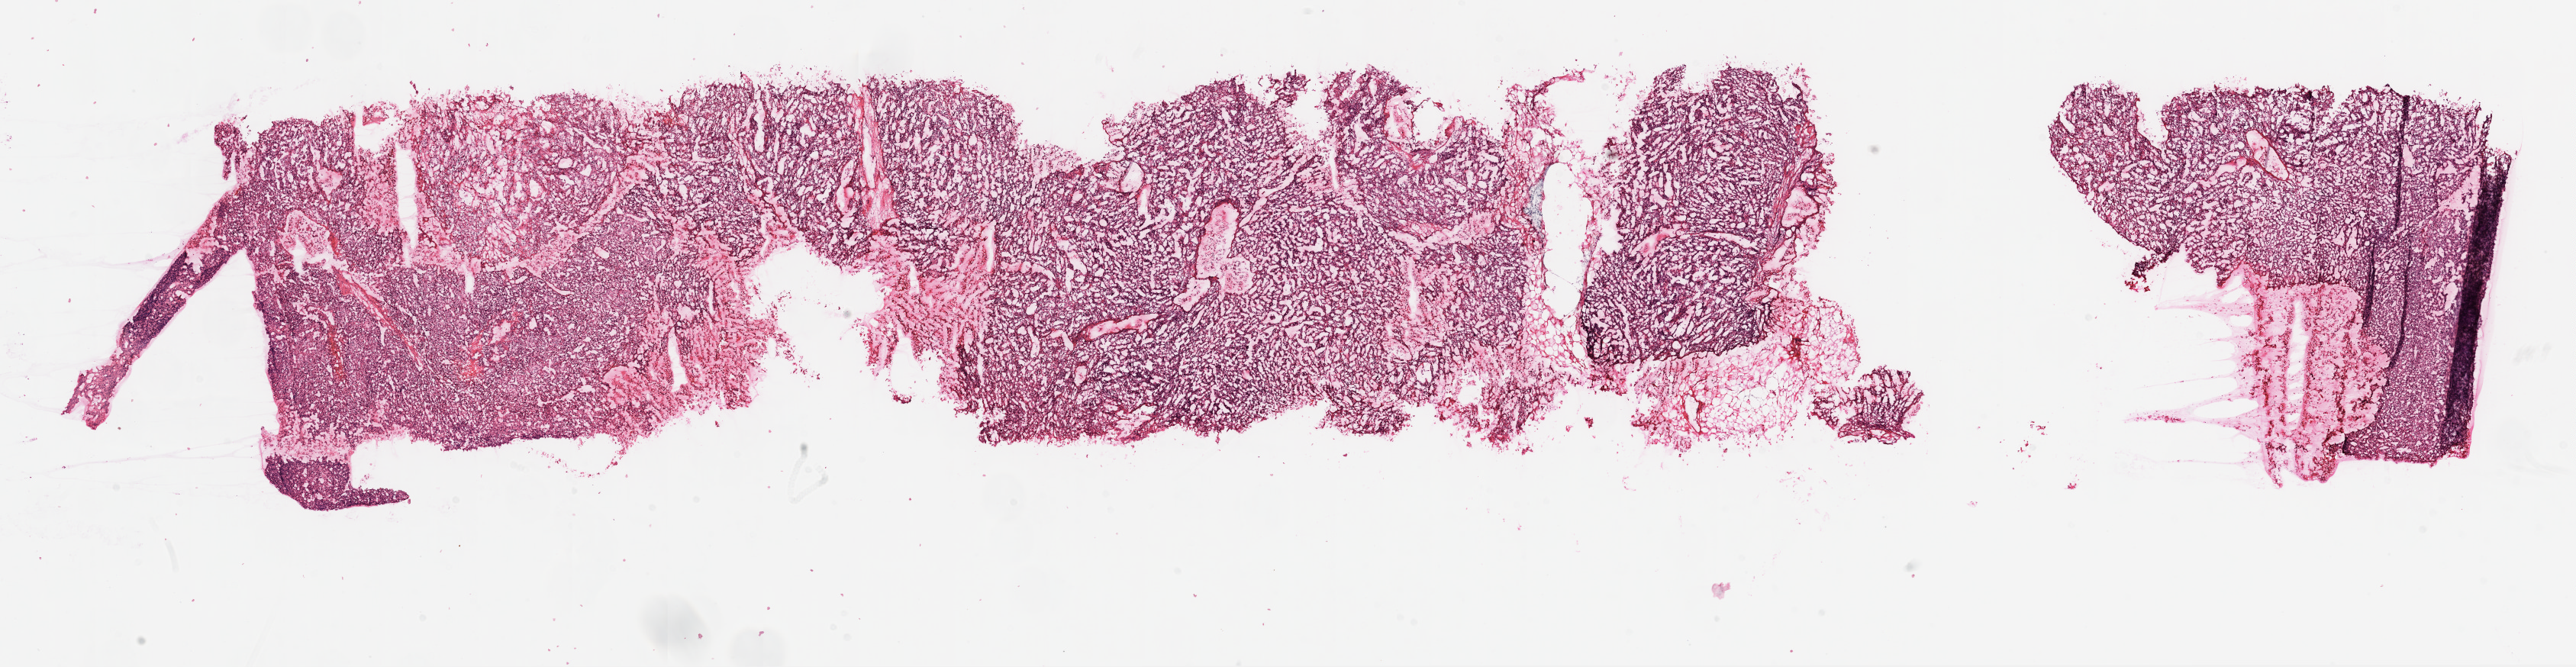
Whole-slide histology image, H&E, whole scanned area (about 27.1 x 7.0 mm, from a 20x scan) shown as a low-resolution overview. Frozen section from the top of the tissue portion. Sample: primary tumour, kidney. Female, age 65 years at initial diagnosis. Histologic grade: G2 (moderately differentiated). Pathologist review of this section (percent, as recorded): tumour cells 90%, tumour nuclei 85%, normal cells 0%, stromal cells 10%, necrosis 0%.
AJCC pathologic stage: I. Diagnosis: Clear cell adenocarcinoma, NOS. Lymph nodes positive (case pathology): 0 of 2 examined.